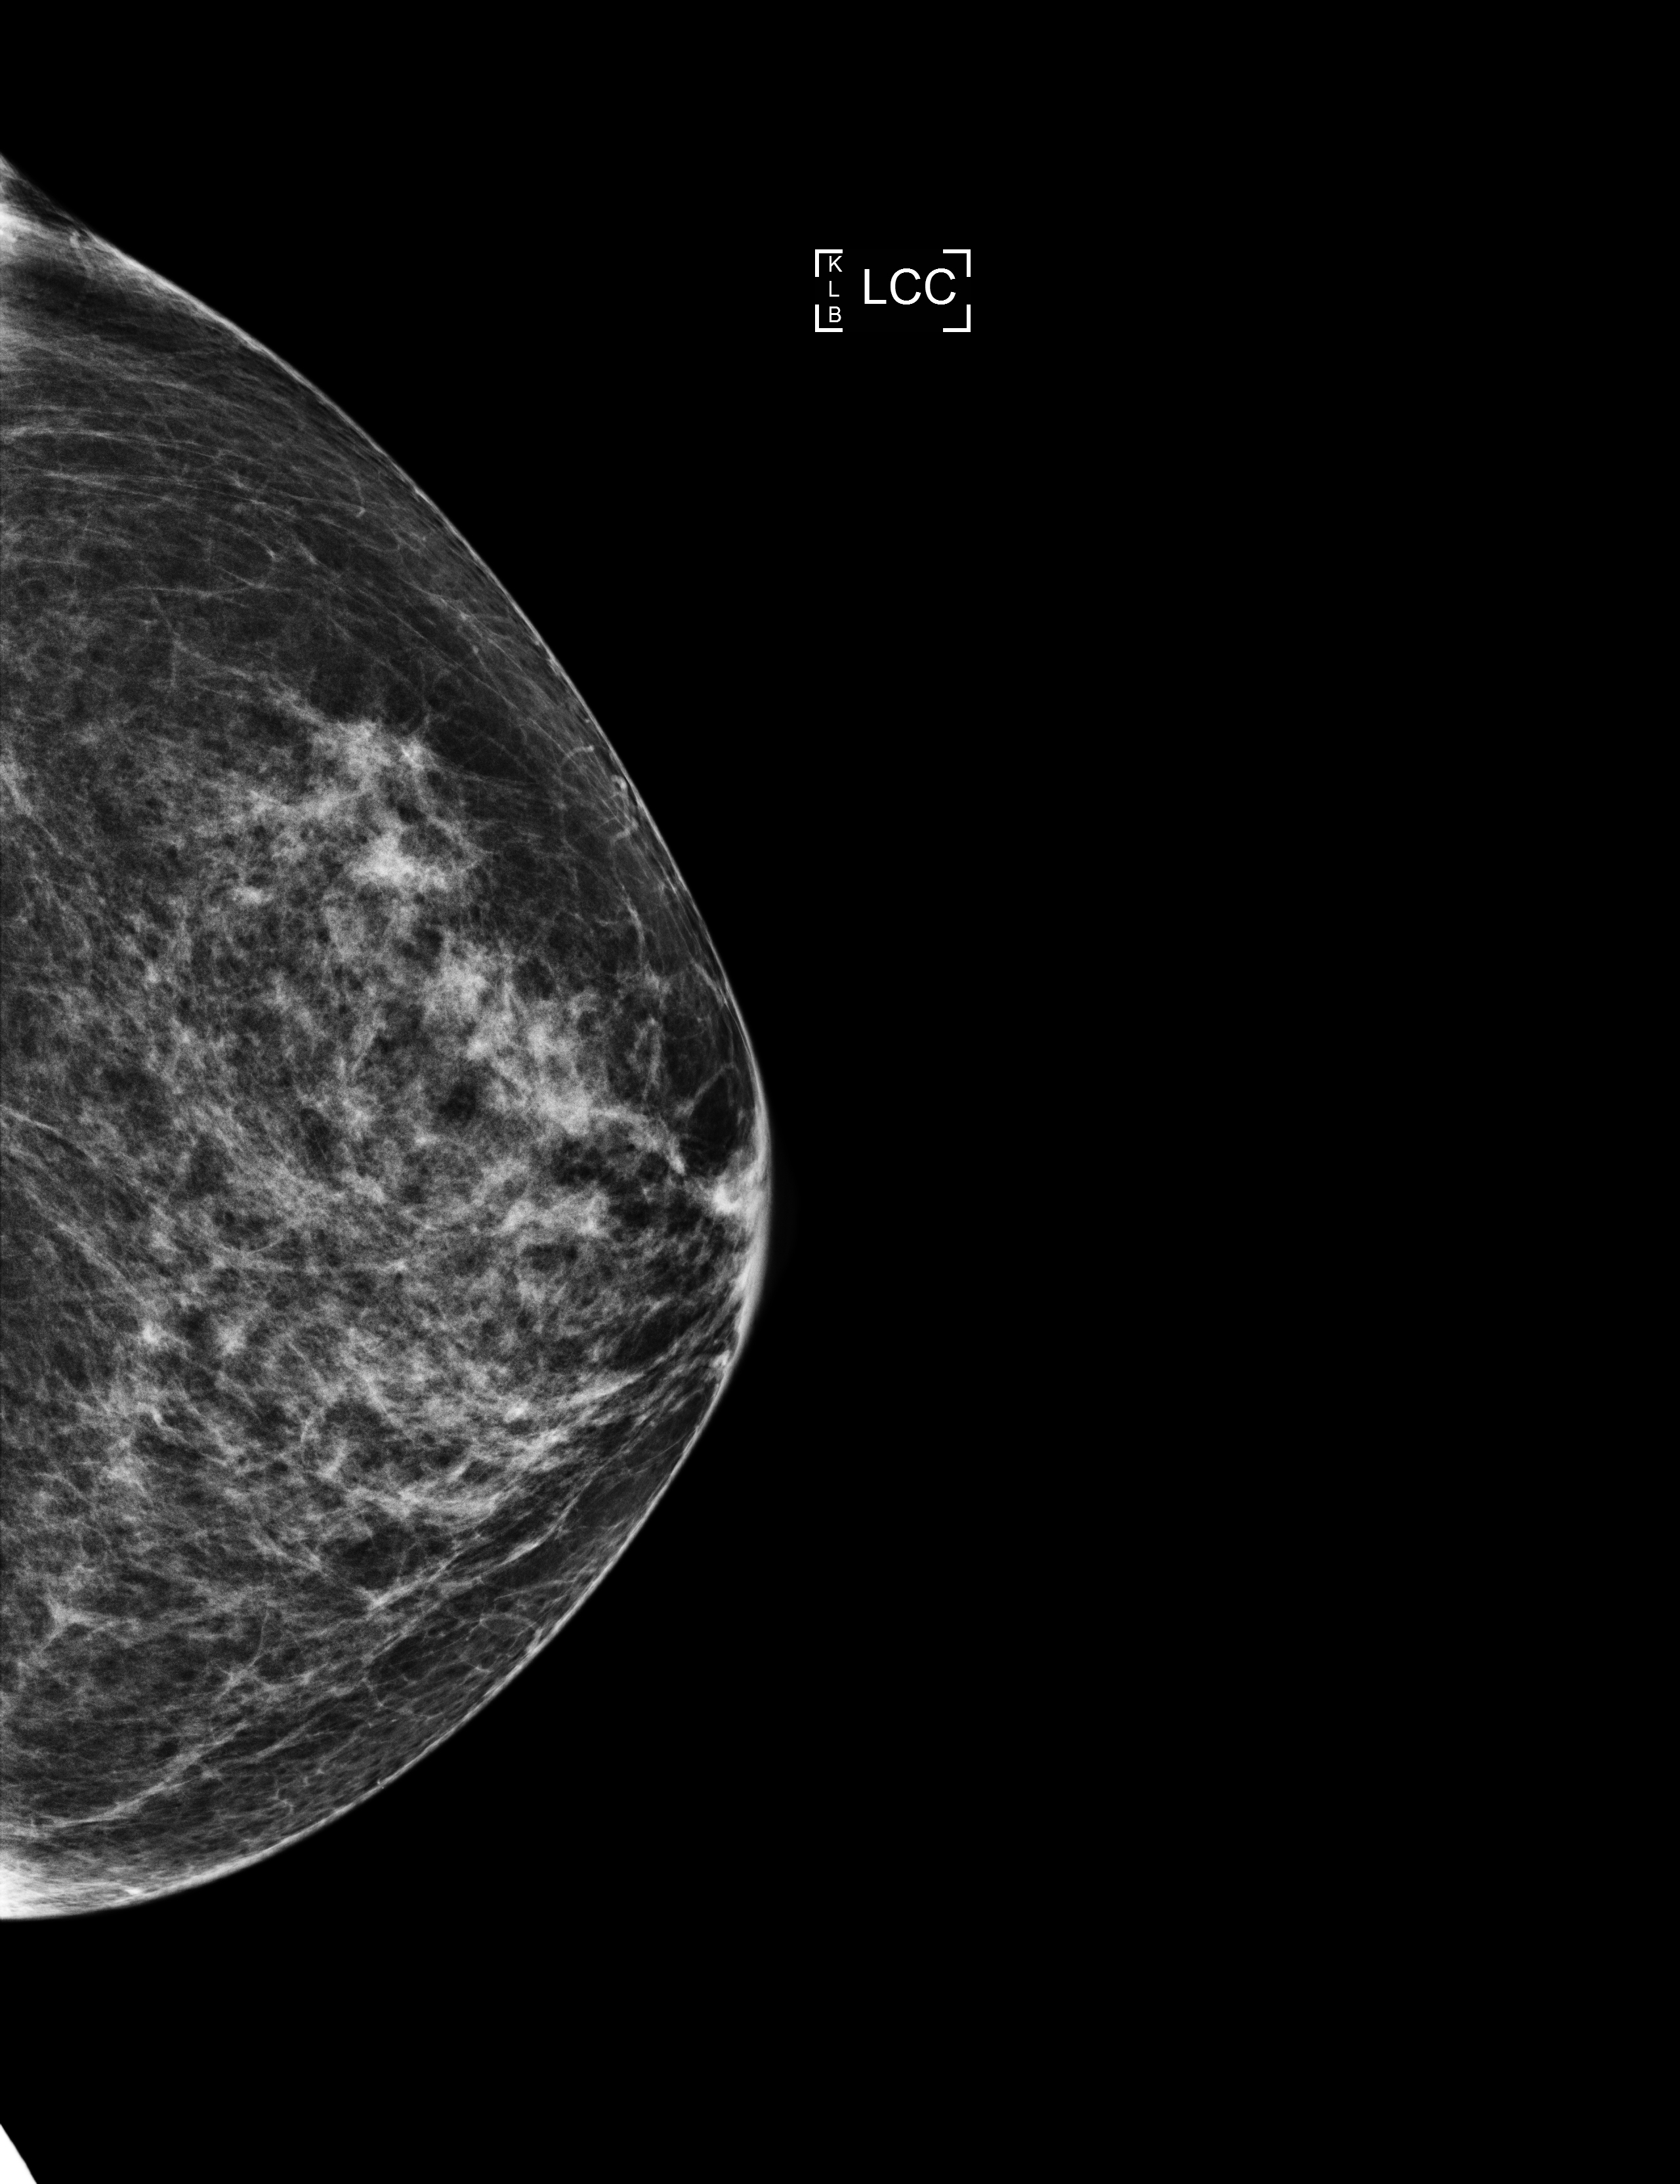
Annual screening mammography examination; compressed breast thickness 63 mm. Female patient, age 64 years.
Image type: full-field digital mammogram. Breast: left. Projection: cranio-caudal projection.